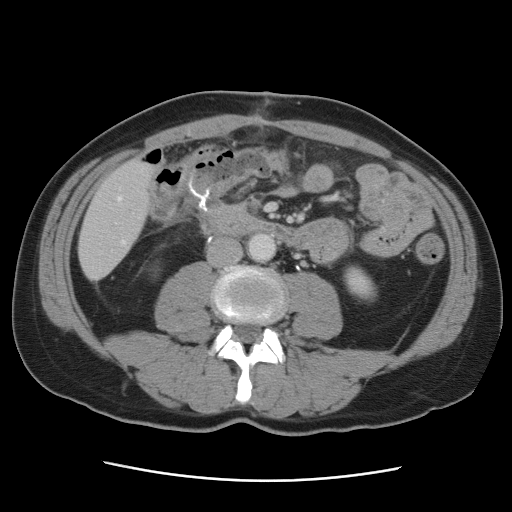
Contrast-enhanced abdominal CT, one axial slice. Slice 16 of 89 in the series (ordered by position). 120 kVp. Soft-tissue window (W 400 / L 40 HU). 512 × 512 image matrix, field of view 366 × 366 mm. Male patient, age 59 years. Case-level facts recorded for this patient, not image findings: diagnosis: colorectal cancer liver metastases, imaged before liver resection; multiple liver metastases: yes; largest metastasis: 0.6 cm; disease in both lobes: yes.
Annotated regions visible in this slice (manually delineated by an expert):
- hepatic veins: bounding box [x1, y1, x2, y2] px = [118, 197, 125, 244]
- liver: [79, 160, 157, 280]
- planned liver remnant (the part of the liver to remain after resection): [79, 159, 157, 257]